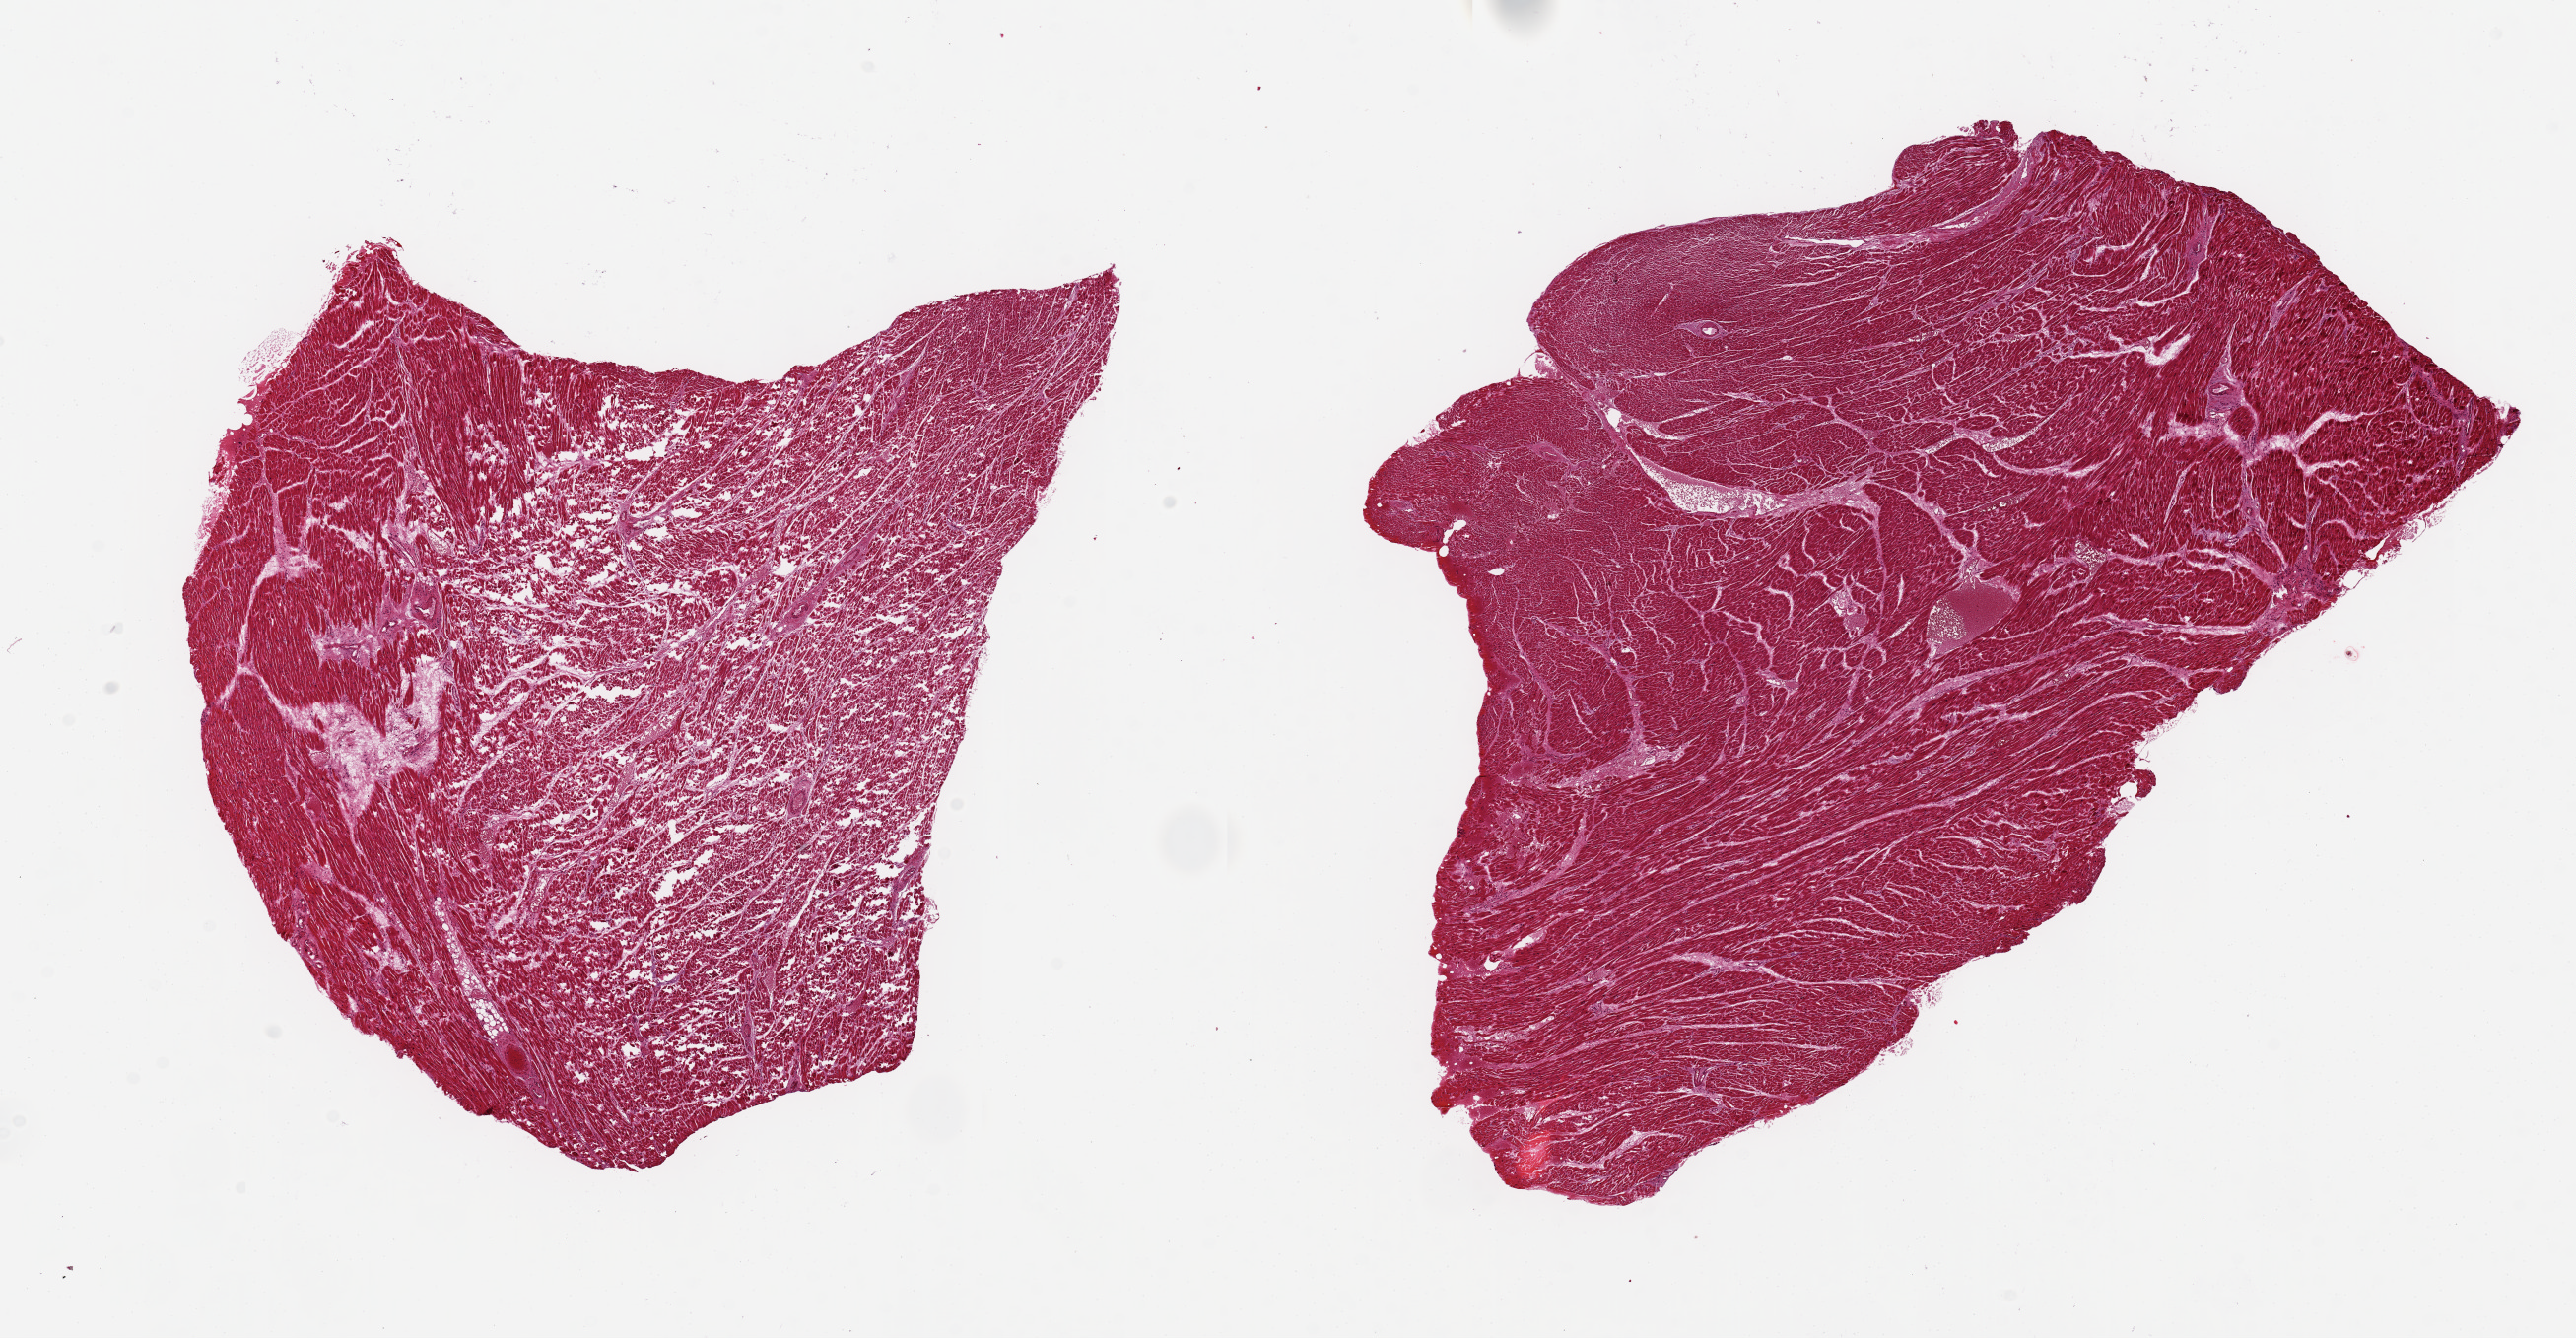
Whole-slide image, H&E stain — low-resolution overview of the scanned area, about 20.7 x 10.7 mm (acquisition: 20x scan); PAXgene-fixed, paraffin-embedded tissue; section of heart (target tissue); tissue donor sample.
Pathologist's review note for this sample: 2 pieces, 10x6 & 6x6 mm.